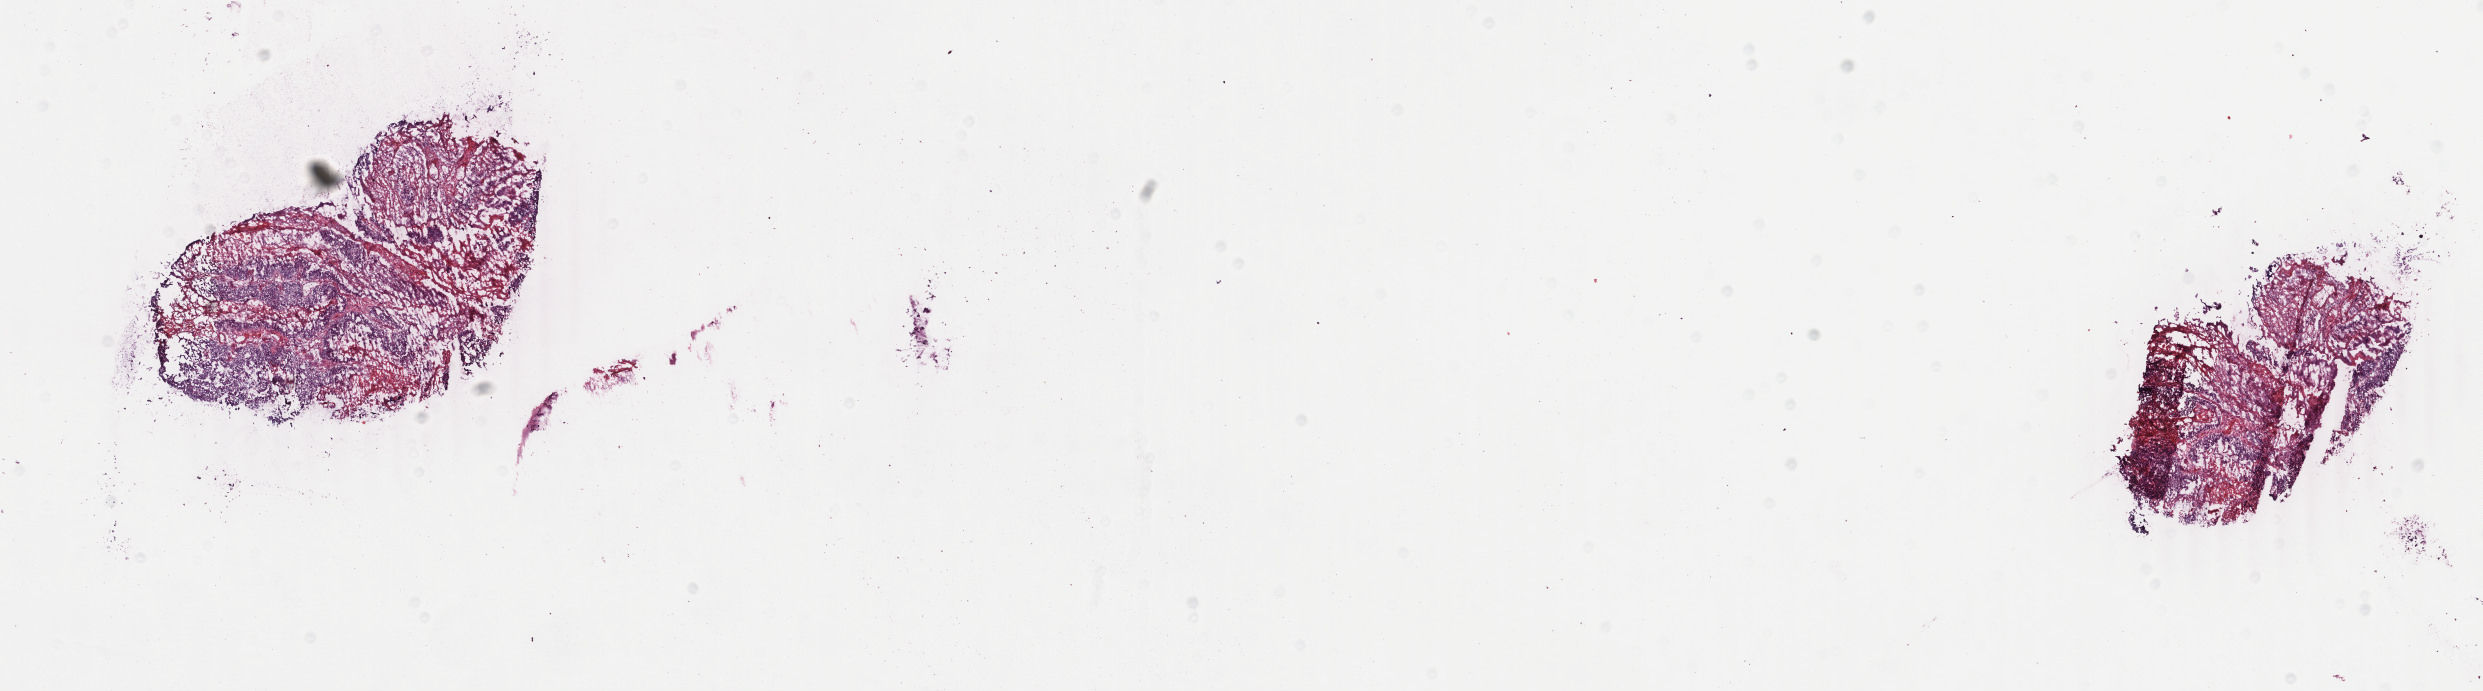
Digitized H&E-stained tissue section (whole slide) — a low-resolution overview of the entire scanned area, about 19.8 x 5.5 mm, frozen section from the bottom of the tissue portion, rectum, primary tumour sample. Male patient; age at initial diagnosis 66 years. Composition of this section per pathologist review: tumour cells 25%, tumour nuclei 80%, normal cells 0%, stromal cells 15%, necrosis 60%. Inflammatory infiltration, as recorded: lymphocyte infiltration 5%, monocyte infiltration 0%, neutrophil infiltration 1%.
AJCC pathologic stage: II (5th edition). Lymph nodes positive (case pathology): 0 of 15 examined. Diagnosis: Adenocarcinoma, NOS.